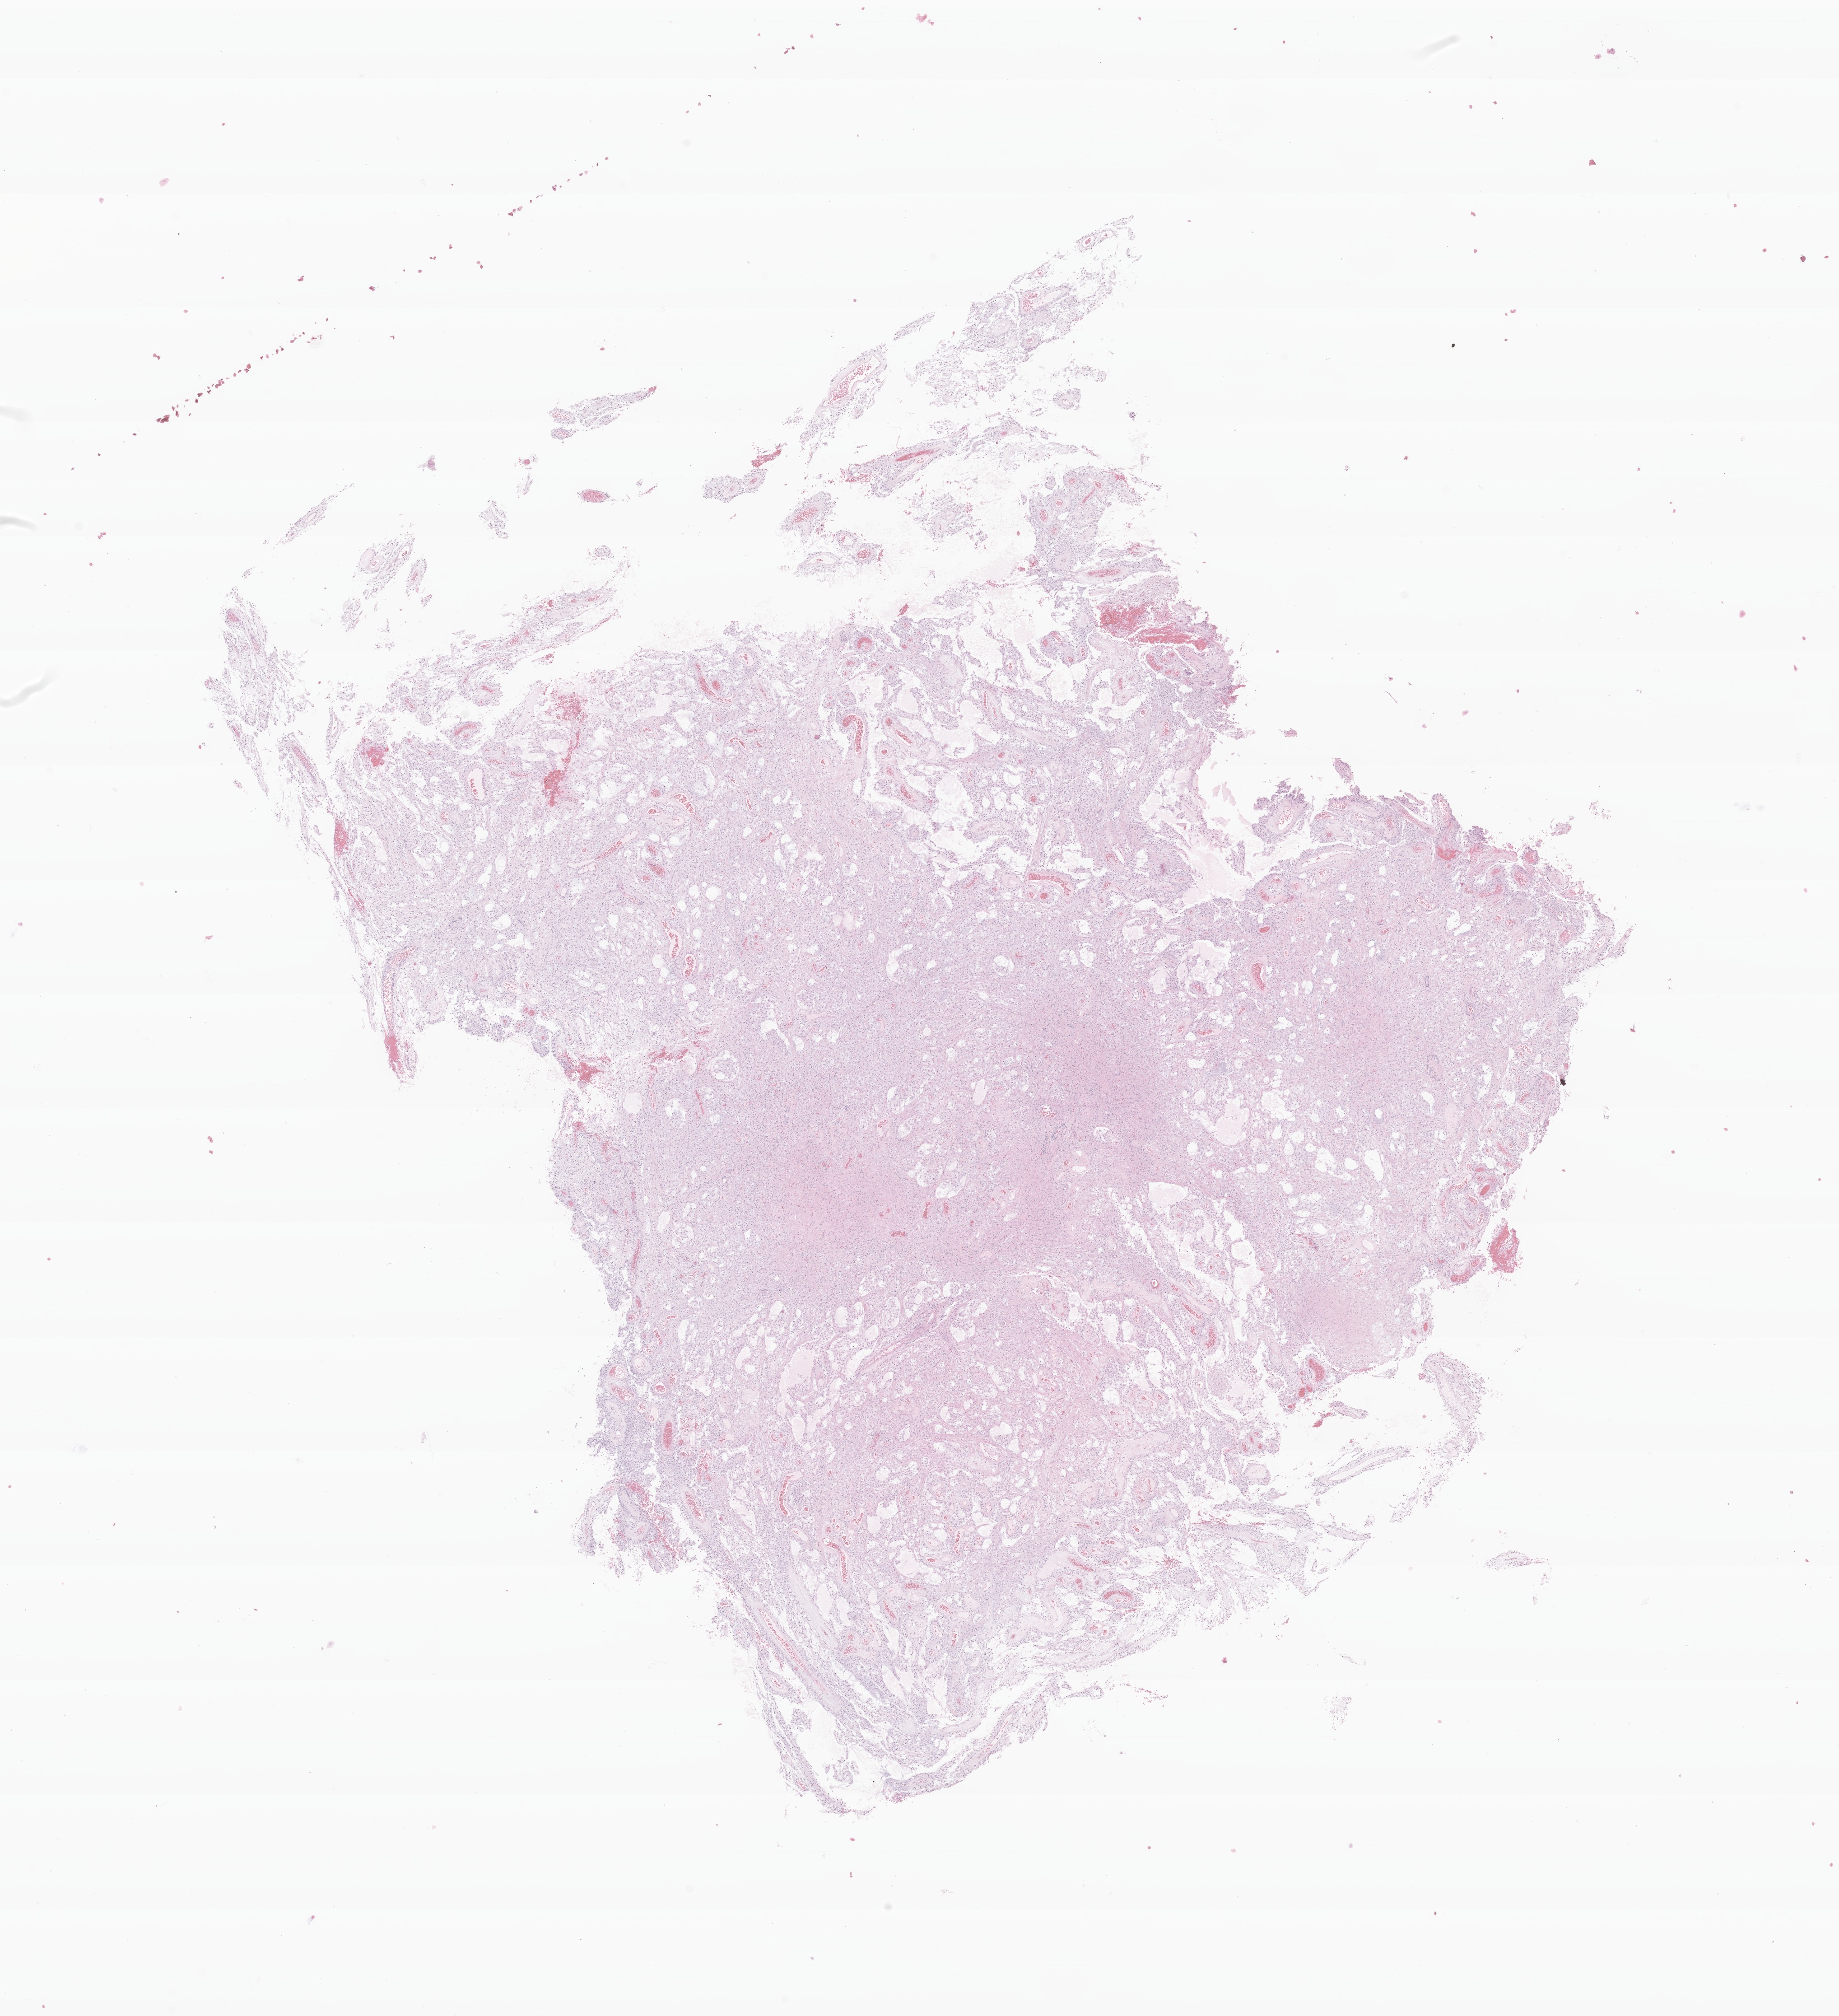
H&E whole-slide image of tumor tissue from the brain — a low-resolution overview of the entire scanned area, about 17.1 x 18.8 mm; formalin-fixed, paraffin-embedded (FFPE) tissue. Female patient, age 77 months (6 years 5 months).
Diagnosis (ICD-O-3 morphology term): Pilocytic astrocytoma.